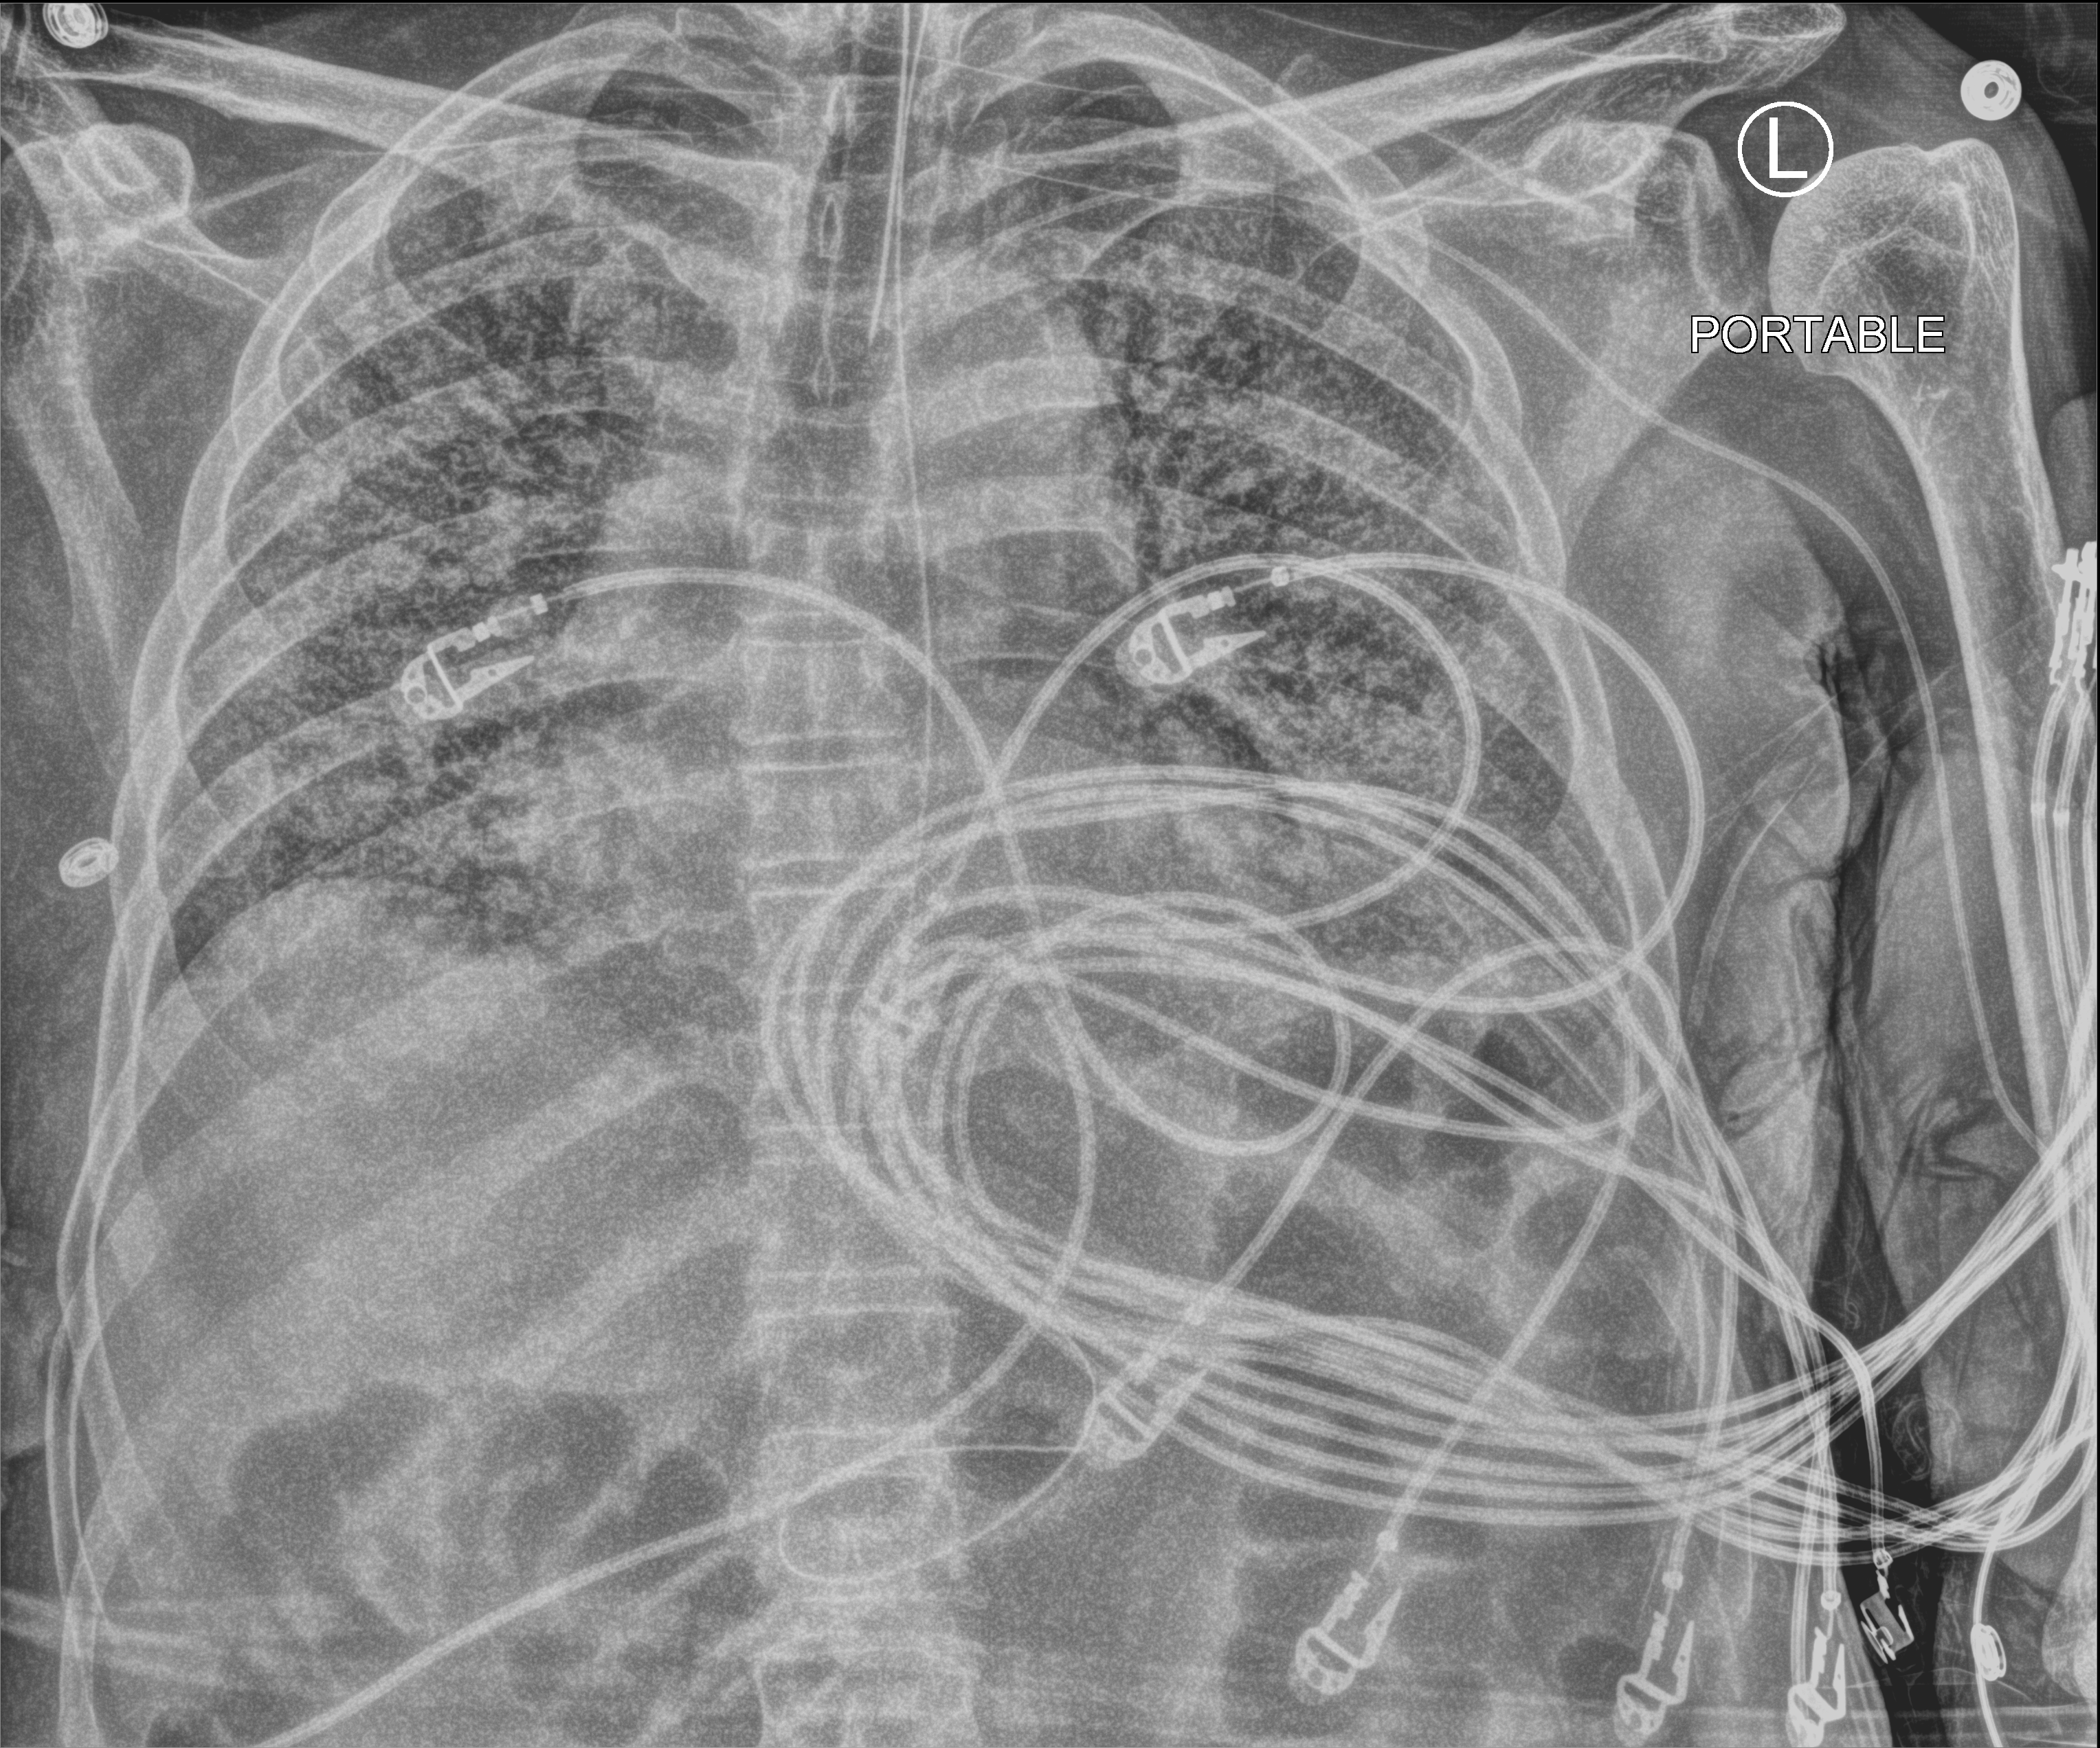
Chest X-ray (portable). Patient hospitalised with COVID-19; male, aged 60–74 years.
Hospital-stay facts (about this admission, not read from this image; timing relative to this image not recorded):
- admitted to intensive care during this hospital stay: yes